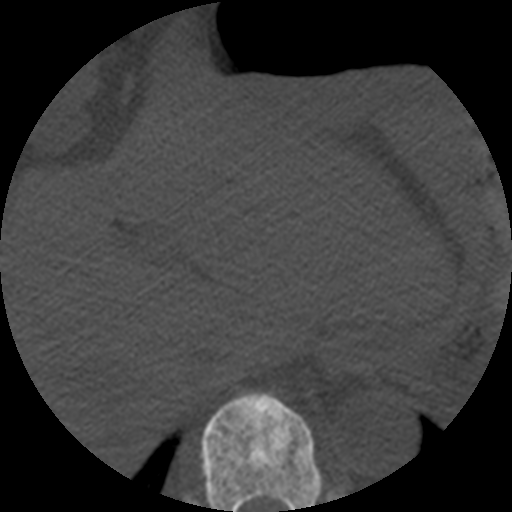
CT including the spine, one axial slice; slice 268 of 508 in the series (ordered by position); 120 kVp; bone window (W 1800 / L 400 HU); 1.25 mm slice thickness; 512 × 512 image matrix. Patient age 57 years. From the clinical record (not read from this slice): primary cancer: prostate.
Structures marked on this image (semi-automatically segmented with operator editing):
- T10 vertebra: bounding box (x1, y1, x2, y2) in pixels: (201, 391, 322, 512)